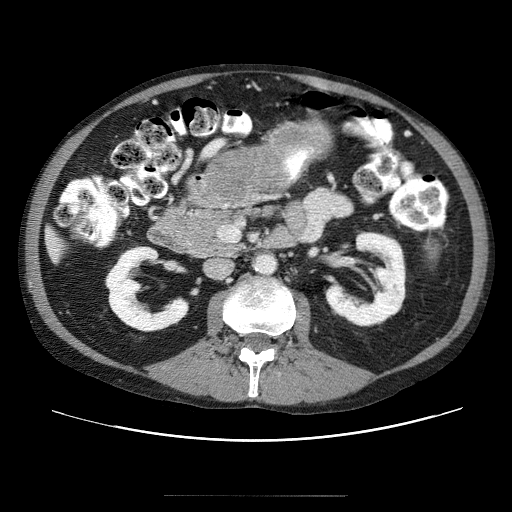
Contrast-enhanced abdominal CT (liver protocol), one axial slice; position 1 of 69 along the scan axis; soft-tissue window (W 400 / L 40 HU); 2.5 mm slice thickness; 512 × 512 image matrix. Case-level facts recorded for this patient, not image findings: diagnosis: hepatocellular carcinoma (patient treated with transarterial chemoembolisation; whether this scan precedes or follows treatment is not stated here); TNM stage (as recorded): Stage-IVB; Child-Pugh class: B.
Outlined on this slice (semi-automatic segmentation, software-assisted and operator-edited):
- liver parenchyma outside the tumour (the mass and vessels are separate outlines, so this box may not span the whole liver): bounding box <46,236,58,259> (left, top, right, bottom; pixels)
- mass: <205,155,267,203>